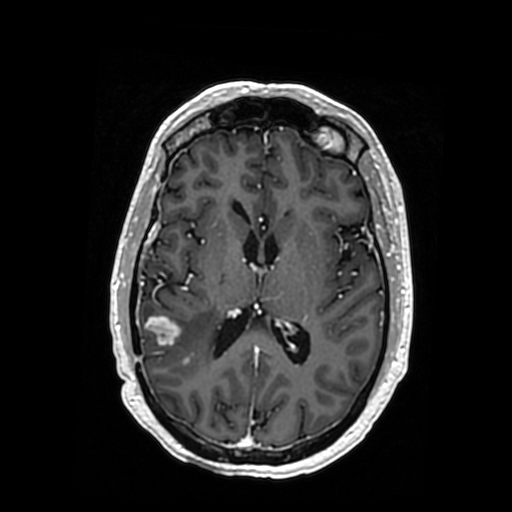
Brain MRI from a brain-tumour surgery series, one axial slice. Slice 171 of 364 in the series (ordered by position). T1-weighted post-contrast. 0.5 mm slice thickness. 512 × 512 image matrix, field of view 260 × 260 mm. From the clinical record (not read from this slice): histopathology: Oligodendroglioma; WHO grade: 3; IDH mutation: yes.
Annotated regions visible in this slice (manually delineated by an expert):
- tumour: box from (x=146, y=315) to (x=217, y=372) px